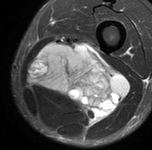
MRI of an extremity soft-tissue mass, one axial slice. Slice 38 of 90 in the series (ordered by position). STIR. MR volume resampled by the dataset authors to the PET/CT grid (not the native acquisition matrix). 152 × 150 image matrix, field of view 148 × 146 mm. Male patient. From the clinical record (not read from this slice): histological type: undifferentiated pleomorphic liposarcoma; grade: high; site of the primary tumour: left thigh.
Outlined on this slice (expert contour drawn on MRI and transferred to this co-registered scan by the dataset authors):
- gross tumour volume including surrounding oedema: bounding box <29,37,126,124> (left, top, right, bottom; pixels)
- gross tumour volume (mass): <32,46,126,122>